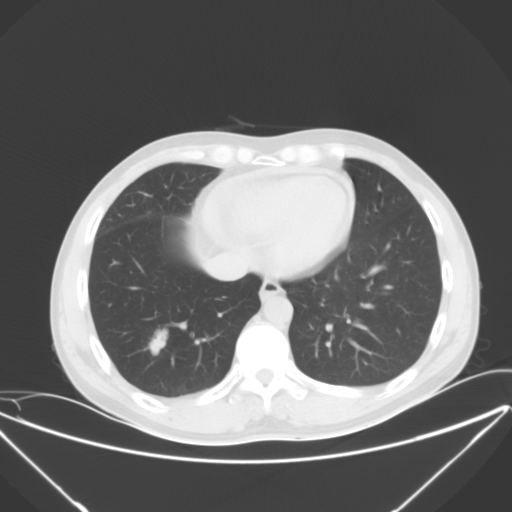
Chest CT, one axial slice. Position 13 of 52 along the scan axis. 120 kVp. Lung window (W 1500 / L -600 HU). 512 × 512 image matrix, field of view 397 × 397 mm. Male patient, age 42 years. Case-level facts recorded for this patient, not image findings: clinical TNM (as recorded): T1b N3 M1b; histopathological grade: G3.
Outlined on this slice (bounding box drawn by a radiologist):
- lung tumour (recorded histology: small cell carcinoma): bounding box [x1, y1, x2, y2] px = [147, 333, 166, 360]